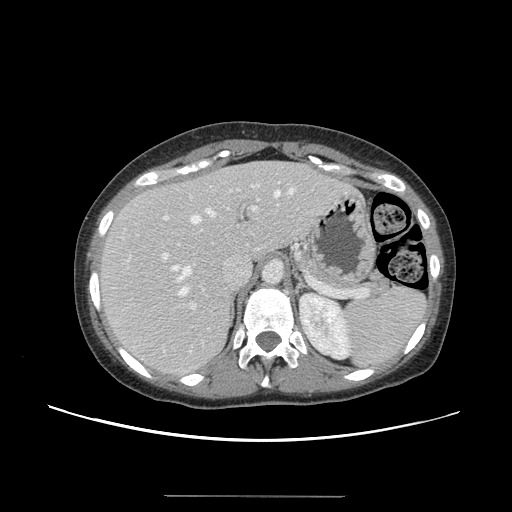
Contrast-enhanced abdominal CT, one axial slice; position 100 of 144 along the scan axis; intravenous contrast given; soft-tissue window (W 400 / L 40 HU); 2.5 mm slice thickness; 512 × 512 image matrix. Female patient, age 53 years. From the clinical record (not read from this slice): diagnosis: colorectal cancer liver metastases, imaged before liver resection; multiple liver metastases: yes; largest metastasis: 1.1 cm; chemotherapy before resection: no.
Outlined on this slice (expert manual segmentation):
- hepatic veins: bounding box <172,188,294,295> (left, top, right, bottom; pixels)
- liver: <100,162,351,376>
- planned liver remnant (the part of the liver to remain after resection): <100,163,304,300>
- portal vein (with intrahepatic branches): <162,181,281,310>